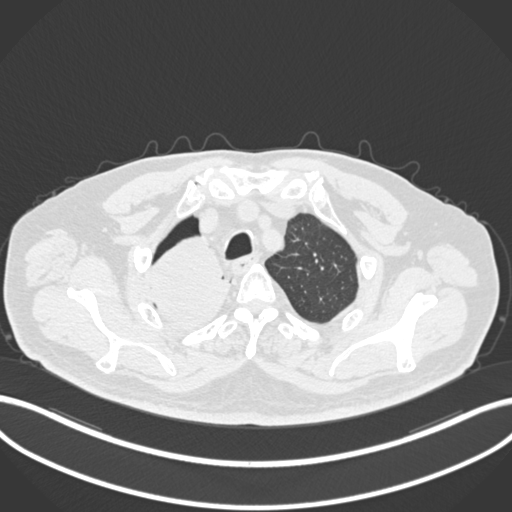
Chest CT, one axial slice. Position 181 of 218 along the scan axis. 120 kVp. Lung window (W 1500 / L -600 HU). 1 mm slice thickness. 512 × 512 image matrix, field of view 400 × 400 mm. Patient: male, 68 years. Case-level facts recorded for this patient, not image findings: clinical TNM (as recorded): T2a N0 M0.
Annotated regions visible in this slice (rectangle marked by the reading radiologist):
- lung tumour (recorded histology: adenocarcinoma): bounding box <145,234,234,335> (left, top, right, bottom; pixels)